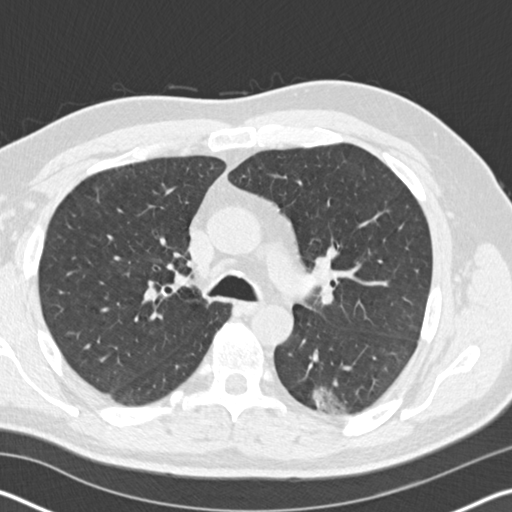
Low-dose screening chest CT, one axial slice; position 113 of 178 along the scan axis; reconstruction kernel B30f; lung window (W 1500 / L -600 HU); 2 mm slice thickness; 512 × 512 image matrix.
Annotated regions visible in this slice (outlined manually by an expert reader):
- lesion 1 (tumor, lower lobe of left lung): bounding box <313,387,346,414> (left, top, right, bottom; pixels)